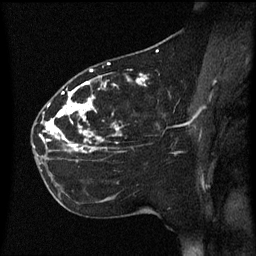
Breast MRI (dynamic contrast-enhanced), one sagittal slice. Slice 31 of 60 in the series (ordered by position). Dynamic contrast-enhanced series, image 2 of 3 at this slice position (ordered by acquisition). 1.5 T. TE 4.2 ms, TR 8.4 ms. 2.2 mm slice thickness. 256 × 256 image matrix, field of view 200 × 200 mm. Female patient, age 35 years. Case-level facts recorded for this patient, not image findings: setting: breast cancer imaged before/during neoadjuvant chemotherapy; receptor status: HER2-positive.
Annotated regions visible in this slice (semi-automatic segmentation, software-assisted and operator-edited):
- analysis volume of interest (the breast-tissue region the enhancement analysis was run in; not a lesion): box from (x=32, y=78) to (x=173, y=163) px
- tumour enhancement mask (voxels above the 70 % enhancement threshold inside the analysis volume of interest): (x=40, y=78)–(x=145, y=153)